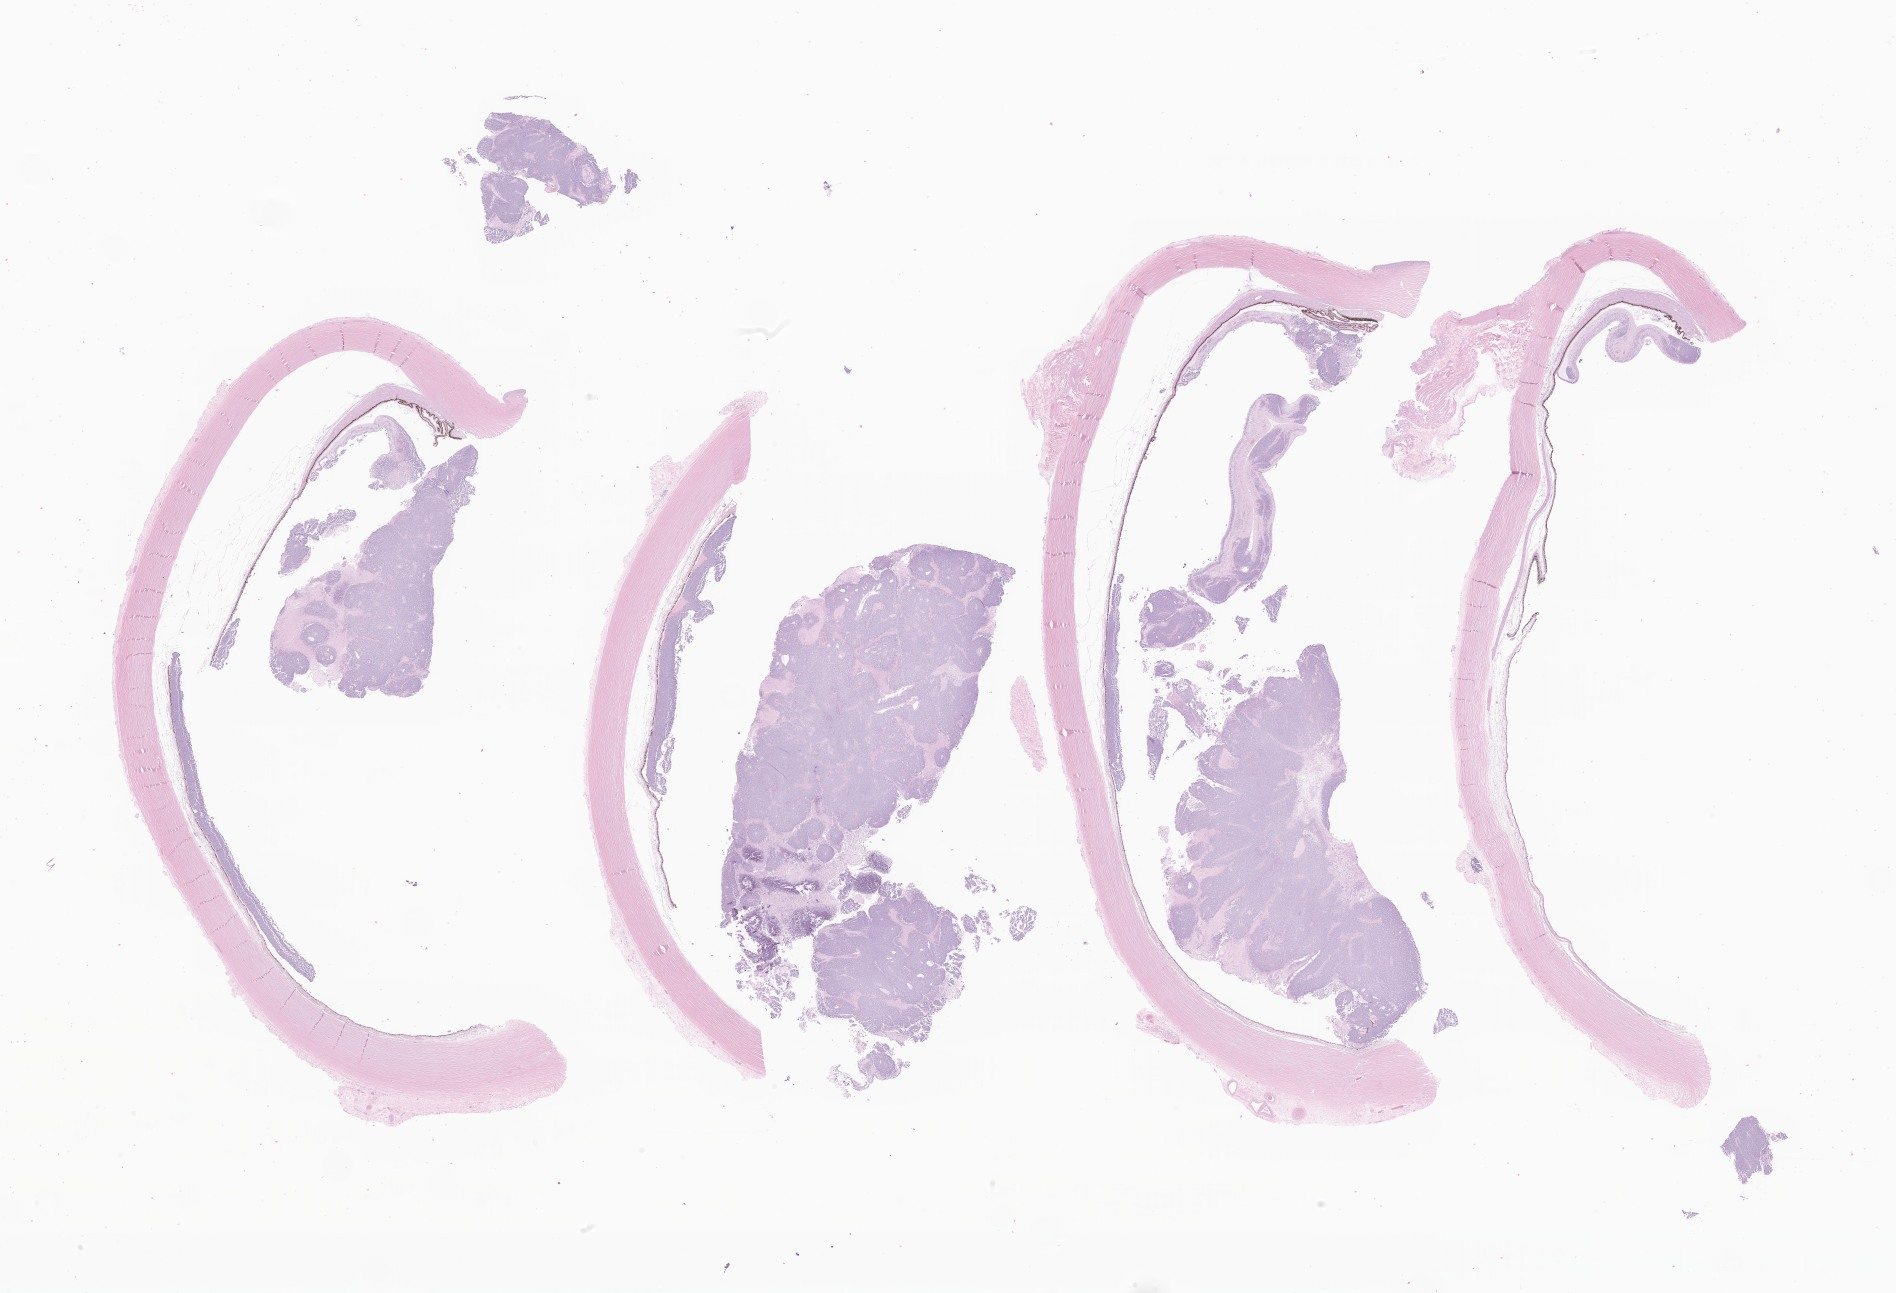
Whole-slide image, hematoxylin and eosin (H&E) stain of tumor tissue from the eye, a low-resolution overview of the entire scanned area, about 32.0 x 21.8 mm; formalin-fixed, paraffin-embedded (FFPE) tissue. Patient: female, age 799 days.
Recorded diagnosis: Retinoblastoma, NOS.